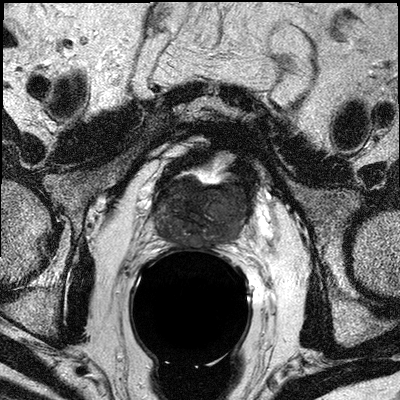
Multiparametric prostate MRI examination; 3 images, each a single mid-volume slice chosen by position (not for content). Treatment context recorded for this patient: Post op patient.
Image 1: T2-weighted axial slice, series "T2W_TSE_AX", slice 17 of 32.
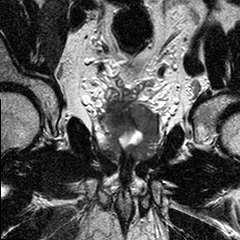
Image 2: coronal T2-weighted image, series "T2W_TSE_COR", slice 13 of 24.
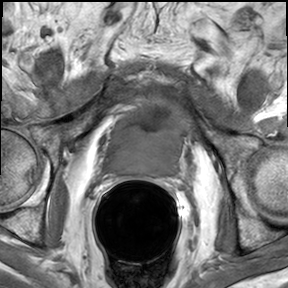
Image 3: DCE (dynamic gadolinium-enhanced) axial slice, slice 17 of 32, dynamic phase 5 of 8.
MRI report (verbatim):
FINDINGS: The prostate has a maximal lateral diameter of 4.6 cm, a maximal craniocaudal diameter of 4.6cm and a maximal AP diameter of 3.3 cm resulting in an estimated gland volume of 36 cc. The zonal anatomy is not preserved, due to history of TURP. There is a large tumor seen involving most of the prostate base, with extension through midthird and apical third, involving the entire left lobe, and most of the right lobe of the prostate at this level and extension into both lobes of the apical third and further extension into the left apex. Imaging findings are suggestive of seminal vesicles infiltration with involvement of the paramedian aspects (base) the right seminal vesicles. There is tumor extension into the periprostatic fat in the midline (in between the seminal vesicles) Se 401 SL 54-57; Se 301 SL 36-42. No evidence for involvement of the neurovascular bundle on either side. No evidence of involvement of bladder neck and rectal wall. No suspiciously enlarged obturator and iliac lymph nodes. Multiplanar reconstructions, subtraction images, and CAD analysis of the dynamic series for assessment of the kinetic information facilitated the interpretation of the exam. IMPRESSION: 1) Large tumor involving approximately 75% of the prostate gland, with extension into left apex. 2) Imaging findings suggestive of manifest seminal vesicles infiltration of the right seminal vesicles base. (Se 401 SL 54-57; Se 301 SL 36-42), and extension into the periprostatic fat tissue between the seminal vesicles (midline). 3) Neuro-vascular bundles not involved. 4) No suspiciously enlarged obturator or iliac lymph nodes

Prostate biopsy pathology (as recorded):
The specimen consists of multiple brown core biopsies ranging from 0.5cm to 1.7cm in length and 0.1cm in diameter. The specimen is submitted in seven cassettes.1-right pz, 2-right pz/tz, 3-right apex, 4-left pz, 5-left pz/tz, 6-left apex, 7-floater. PROSTATE 1-right pz, PROSTATIC ADENOCARCINOMA, GLEASON SCORE 3 + 4 = 7/10, INVOLVING ONE CORE, 50% OF TISSUE. 2-right pz/tz, PROSTATIC ADENOCARCINOMA, GLEASON SCORE 3 + 4 = 7/10, INVOLVING TWO CORES, 80% OF TISSUE. 3-right apex, PROSTATIC ADENOCARCINOMA, GLEASON SCORE 3 + 4 = 7/10, INVOLVING TWO CORES, 30% OF TISSUE. 4-left pz, PROSTATIC ADENOCARCINOMA, GLEASON SCORE 4 + 3 = 7/10, INVOLVING MULTIPLE CORES, 70% OF TISSUE. 5-left pz/tz, PROSTATIC ADENOCARCINOMA, GLEASON SCORE 3 + 4 = 7/10, INVOLVING TWO CORES, 80% OF TISSUE. 6-left apex, PROSTATIC ADENOCARCINOMA, GLEASON SCORE 4 + 4 = 8/10, INVOLVING MULTIPLE CORES, 70% OF TISSUE. 7-floater PROSTATIC ADENOCARCINOMA, GLEASON SCORE 4 + 4 = 8/10, INVOLVING ONE CORES, 90% OF TISSUE